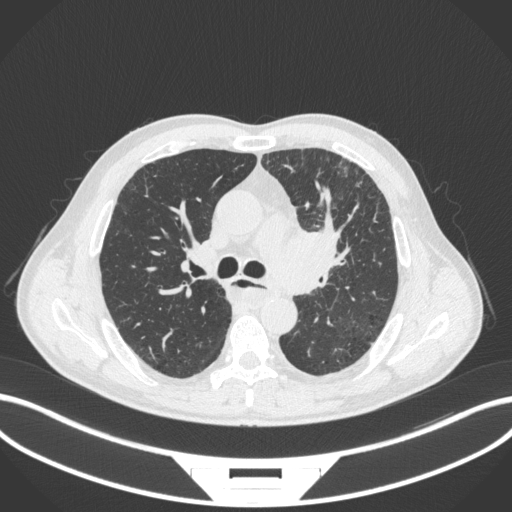
Chest CT, one axial slice. Slice 244 of 411 in the series (ordered by position). Reconstruction kernel B31f. 120 kVp. Lung window (W 1500 / L -600 HU). 1 mm slice thickness. 512 × 512 image matrix, field of view 400 × 400 mm. Male patient, age 57 years. From the clinical record (not read from this slice): clinical TNM (as recorded): T2a N1 M0.
Annotated regions visible in this slice (bounding box drawn by a radiologist):
- lung tumour (recorded histology: squamous cell carcinoma): bounding box <269,221,344,296> (left, top, right, bottom; pixels)